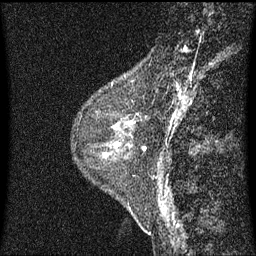
Breast MRI (dynamic contrast-enhanced), one sagittal slice. Slice 17 of 60 in the series (ordered by position). Dynamic contrast-enhanced series, image 2 of 3 at this slice position (ordered by acquisition). 1.5 T. TE 4.2 ms, TR 8 ms. 256 × 256 image matrix. Patient: female, 48 years.
Annotated regions visible in this slice (semi-automatically segmented with operator editing):
- analysis volume of interest (the breast-tissue region the enhancement analysis was run in; not a lesion): bounding box (x1, y1, x2, y2) in pixels: (103, 74, 145, 139)
- tumour enhancement mask (voxels above the 70 % enhancement threshold inside the analysis volume of interest): (112, 114, 138, 137)